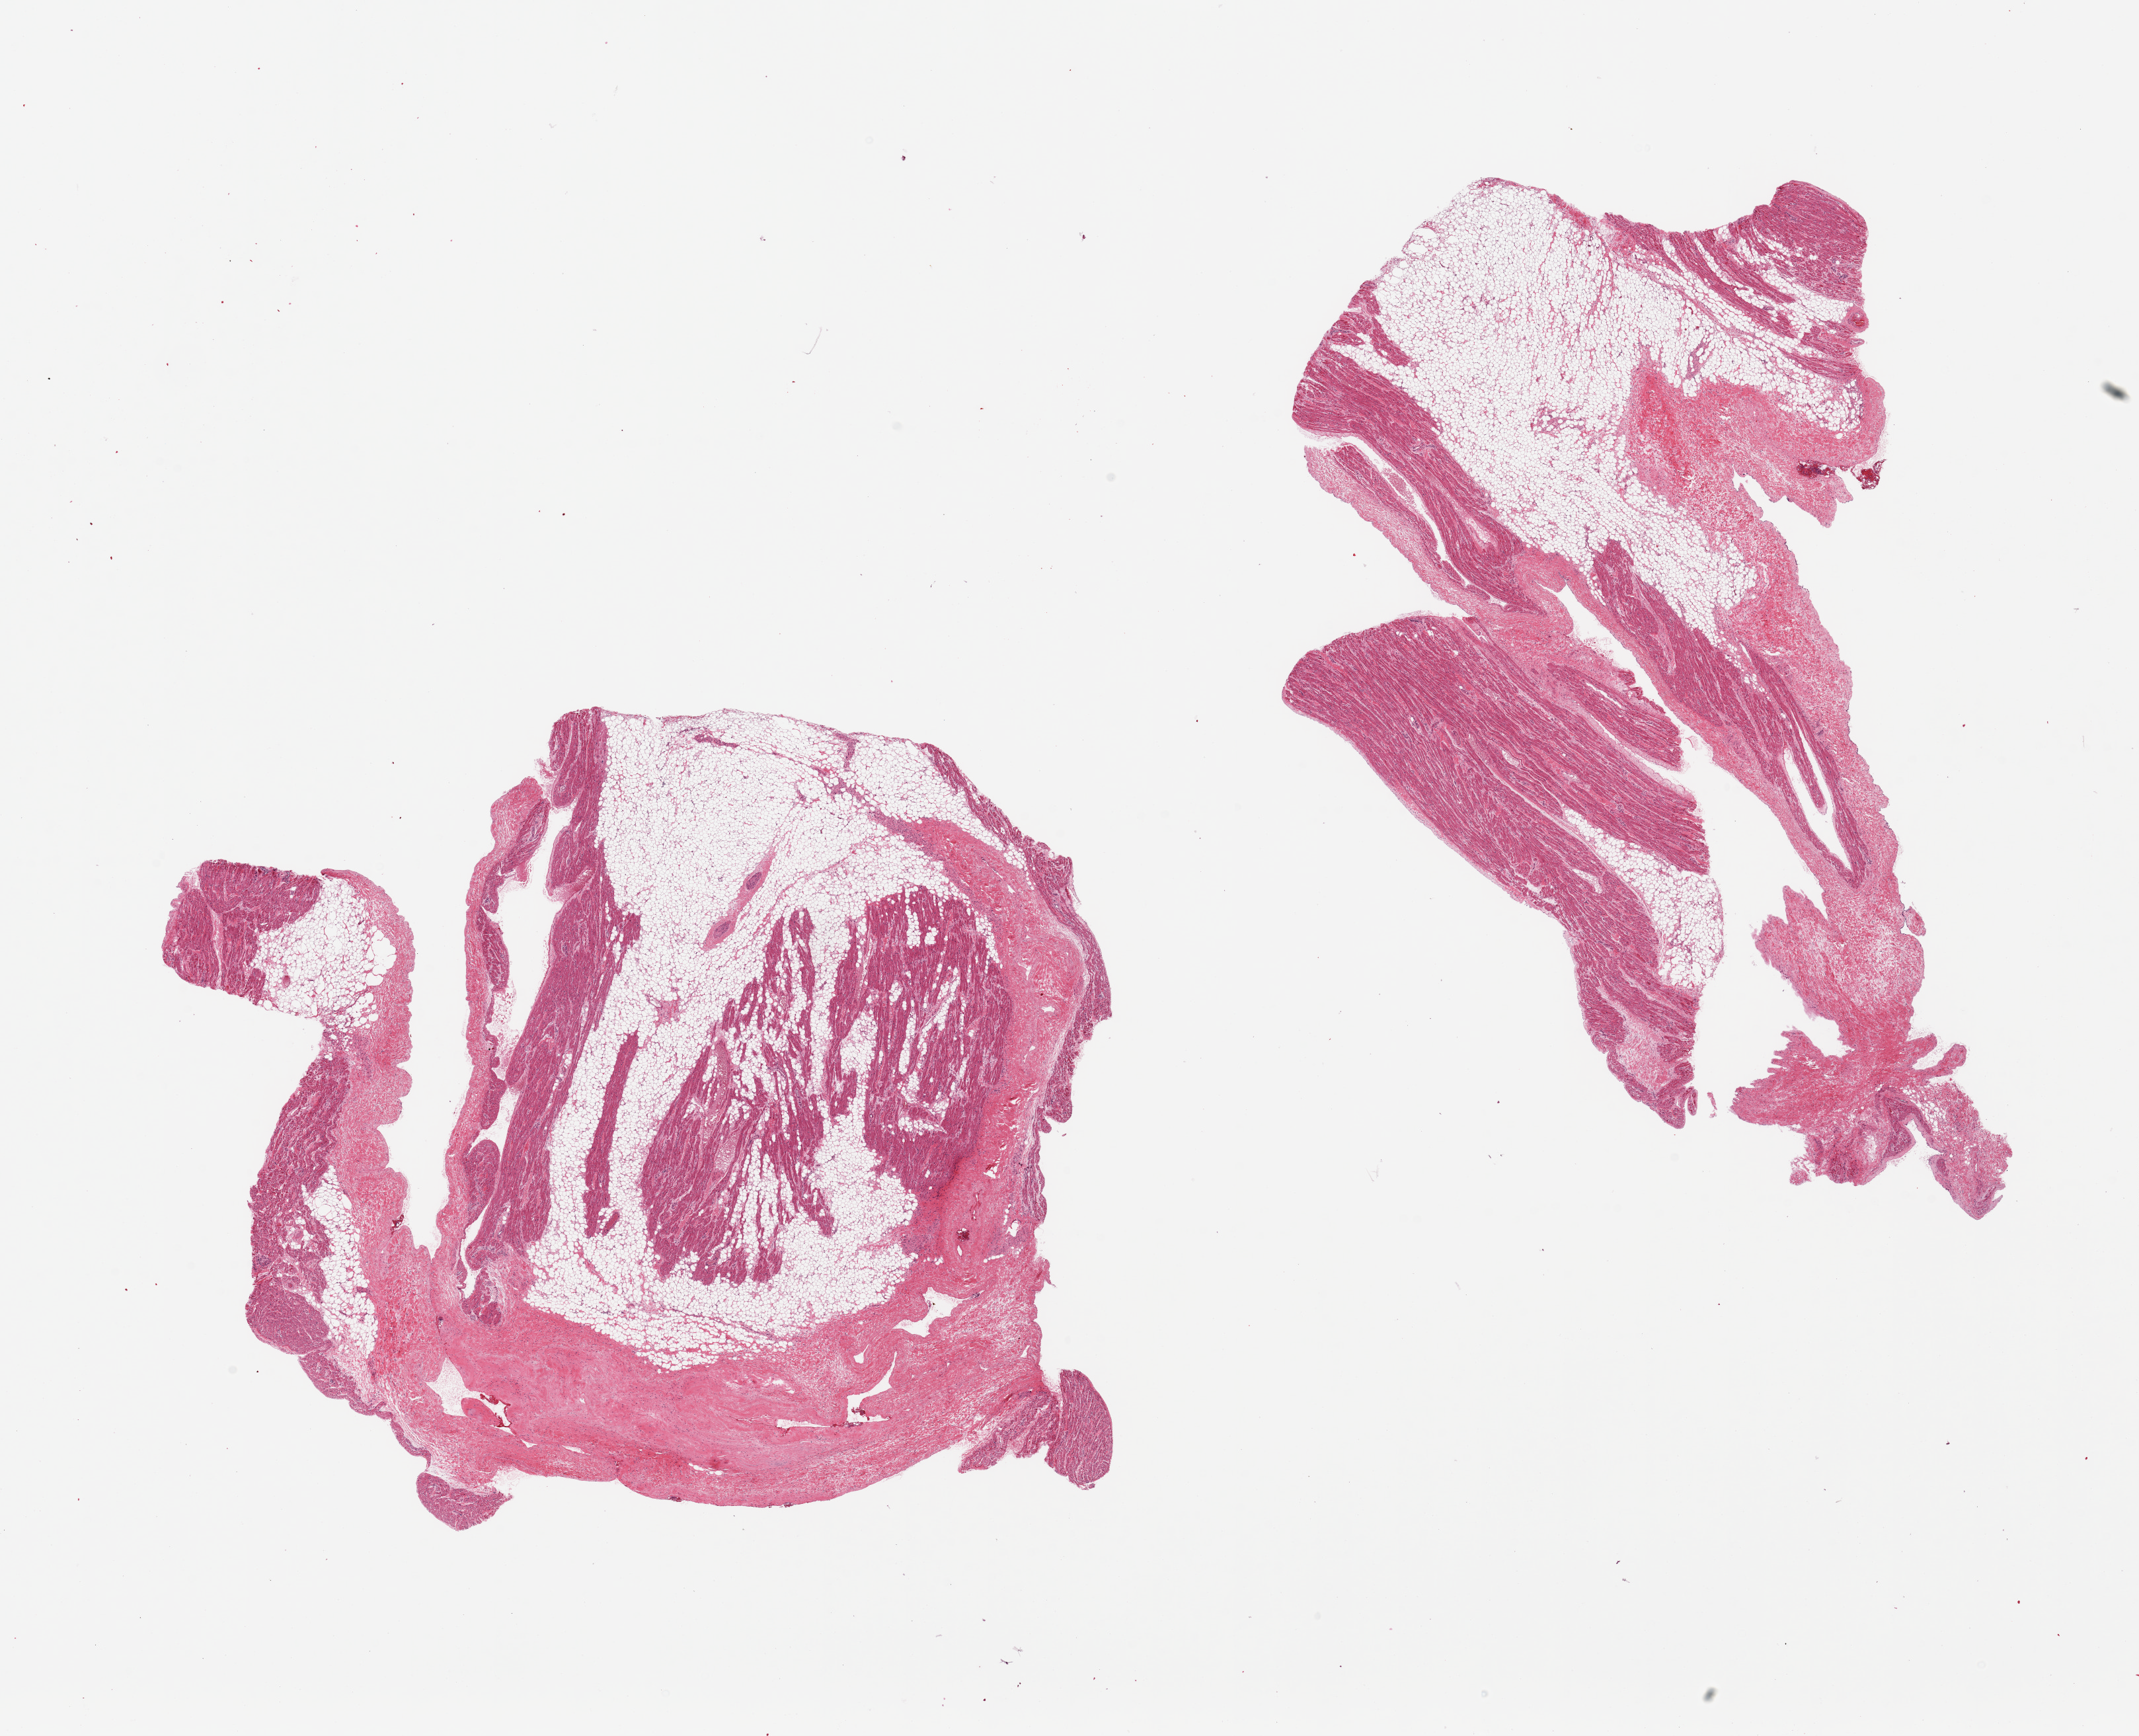
Haematoxylin and eosin whole-slide image, brightfield, a low-resolution overview of the entire scanned area, about 25.6 x 20.8 mm, PAXgene-fixed, paraffin-embedded tissue, target tissue: auricular appendage, tissue donor sample. Donor sex: male.
Pathologist's review note for this sample: 2 pieces. Atrial appendage, NOT heart. 1 piece is 40% muscle, 60% fibroadipose. 2nd piece is 20% muscle, 80% fibroadipose.